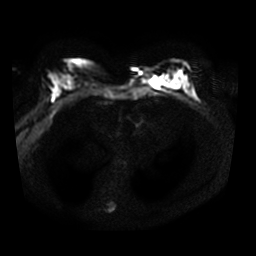
Breast MRI, one axial slice. Slice 20 of 34 in the series (ordered by position). Diffusion-weighted series; image 2 of 4 stored at this slice position (different b-values; order by instance number). 3 T. 5 mm slice thickness. 256 × 256 image matrix, field of view 340 × 340 mm. Female patient.
Annotated regions visible in this slice (manually delineated by an expert):
- tumour on diffusion-weighted imaging: bounding box <150,76,157,86> (left, top, right, bottom; pixels)